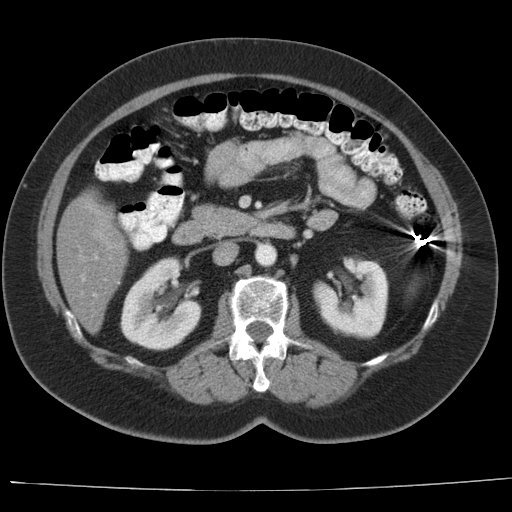
Contrast-enhanced abdominal CT, one axial slice. Slice 9 of 44 in the series (ordered by position). Reconstruction kernel AA-1. Soft-tissue window (W 400 / L 40 HU). 512 × 512 image matrix, field of view 373 × 373 mm. Female patient. From the clinical record (not read from this slice): diagnosis: colorectal cancer liver metastases, imaged before liver resection; multiple liver metastases: yes; largest metastasis: 1.8 cm; disease in both lobes: no.
Structures marked on this image (outlined manually by an expert reader):
- hepatic veins: bounding box (x1, y1, x2, y2) in pixels: (81, 277, 84, 281)
- liver: (58, 195, 128, 332)
- portal vein (with intrahepatic branches): (93, 293, 97, 297)